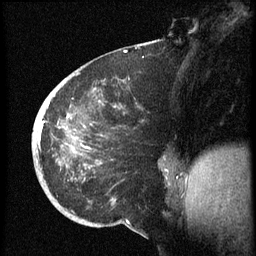
Breast MRI (dynamic contrast-enhanced), one sagittal slice. Position 26 of 60 along the scan axis. Dynamic contrast-enhanced series, image 2 of 3 at this slice position (ordered by acquisition). 1.5 T. TE 4.2 ms, TR 8.4 ms. 256 × 256 image matrix, field of view 200 × 200 mm. Patient: female, 38 years. Case-level facts recorded for this patient, not image findings: setting: breast cancer imaged before/during neoadjuvant chemotherapy; receptor status: HER2-positive.
Structures marked on this image (semi-automatically segmented with operator editing):
- analysis volume of interest (the breast-tissue region the enhancement analysis was run in; not a lesion): box from (x=33, y=74) to (x=173, y=202) px
- tumour enhancement mask (voxels above the 70 % enhancement threshold inside the analysis volume of interest): (x=36, y=103)–(x=102, y=169)